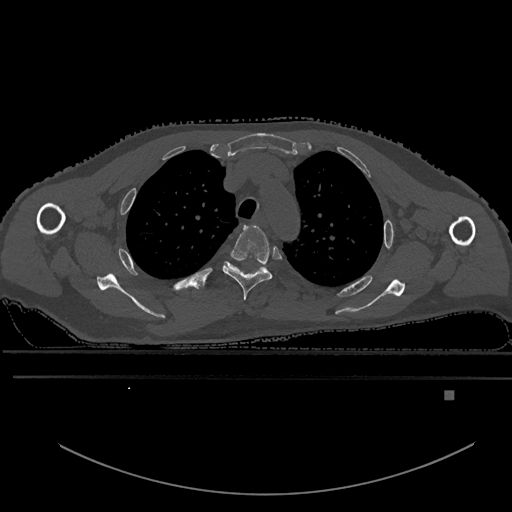
CT including the spine, one axial slice; position 445 of 969 along the scan axis; bone window (W 1800 / L 400 HU); 0.5 mm slice thickness; 512 × 512 image matrix, field of view 456 × 456 mm. Male patient, age 82 years. Case-level facts recorded for this patient, not image findings: primary cancer: prostate; vertebrae with lytic lesions (as recorded): T11, T9, T8, T2.
Outlined on this slice (semi-automatically segmented with operator editing):
- T3 vertebra: bounding box (x1, y1, x2, y2) in pixels: (222, 224, 272, 300)
- T4 vertebra: (226, 262, 267, 271)